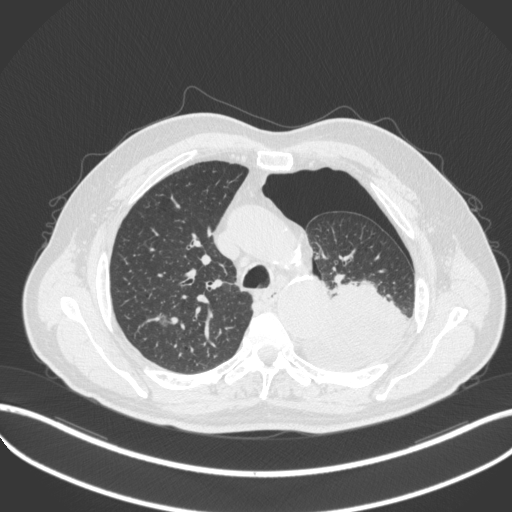
Chest CT, one axial slice. Slice 366 of 466 in the series (ordered by position). Lung window (W 1500 / L -600 HU). 1 mm slice thickness. 512 × 512 image matrix, field of view 400 × 400 mm. Patient: male, 76 years. From the clinical record (not read from this slice): clinical TNM (as recorded): T3 N0 M1b.
Outlined on this slice (rectangle marked by the reading radiologist):
- lung tumour (recorded histology: adenocarcinoma): bounding box <303,280,414,370> (left, top, right, bottom; pixels)